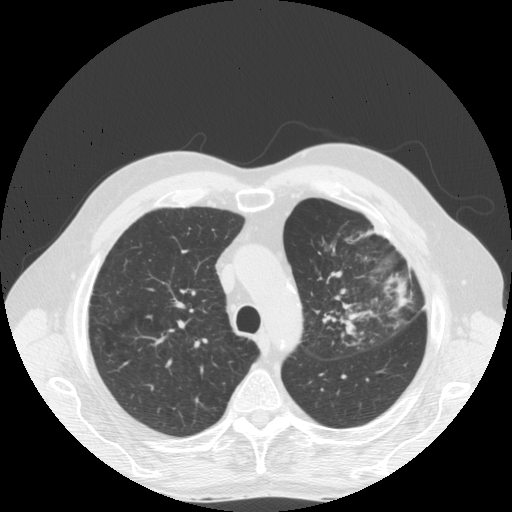
Low-dose screening chest CT, one axial slice. Position 130 of 170 along the scan axis. Reconstruction kernel STANDARD. 140 kVp. Lung window (W 1500 / L -600 HU). 2.5 mm slice thickness. 512 × 512 image matrix.
Outlined on this slice (expert manual segmentation):
- lesion 1 (tumor, upper lobe of left lung): bounding box (x1, y1, x2, y2) in pixels: (340, 293, 356, 336)